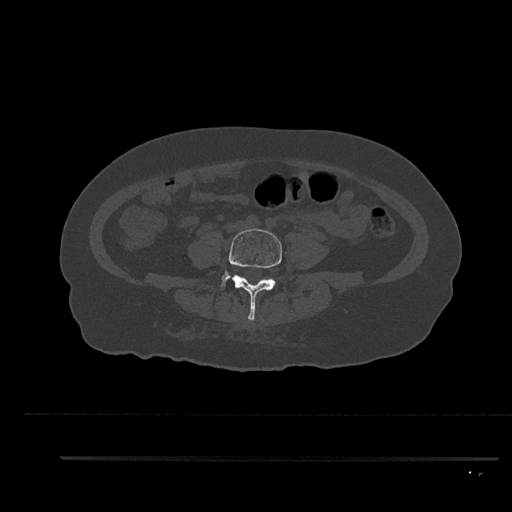
CT including the spine, one axial slice; slice 14 of 797 in the series (ordered by position); reconstruction kernel Br40s/3; bone window (W 1800 / L 400 HU); 0.5 mm slice thickness; 512 × 512 image matrix, field of view 408 × 408 mm. Patient: female, 44 years. Case-level facts recorded for this patient, not image findings: primary cancer: renal.
Structures marked on this image (semi-automatically segmented with operator editing):
- L4 vertebra: bounding box [x1, y1, x2, y2] px = [220, 228, 282, 321]